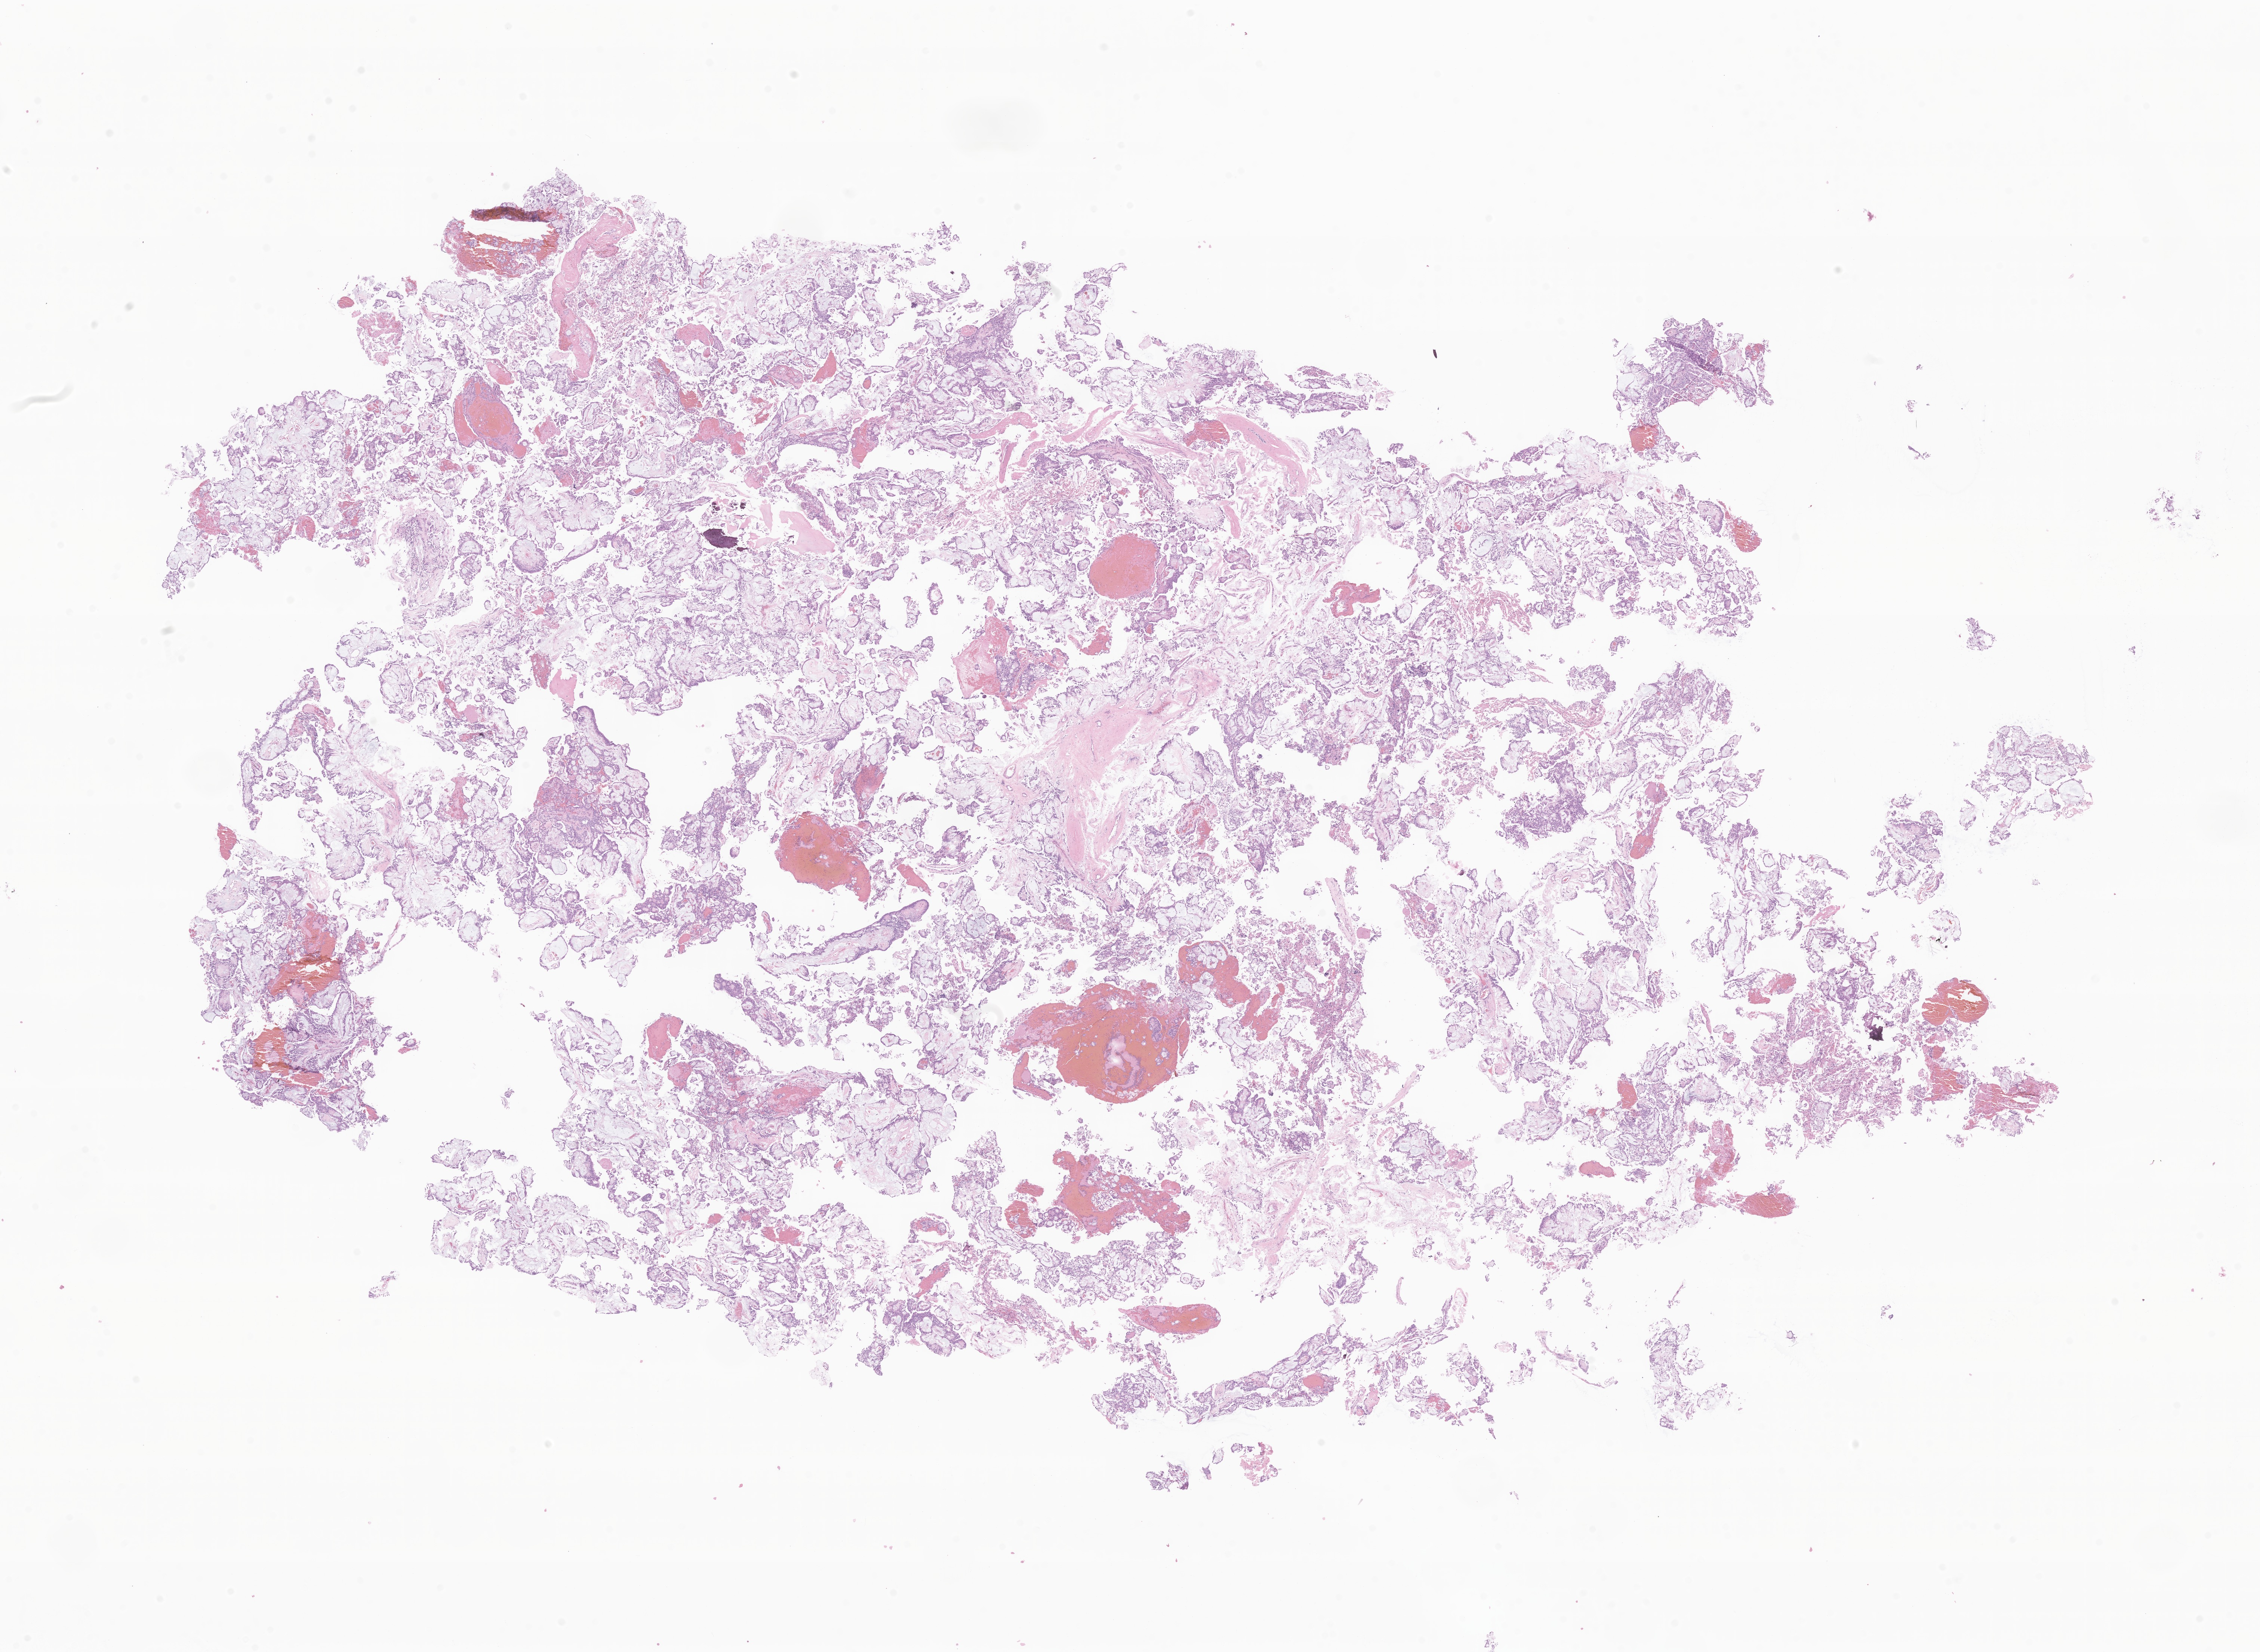
Whole-slide image, hematoxylin and eosin (H&E) stain of tumor tissue from the spinal cord — low-resolution overview of the scanned area, about 25.5 x 18.6 mm, FFPE section. Patient female; age 177 months (14 years 9 months).
Recorded diagnosis: Myxopapillary ependymoma.